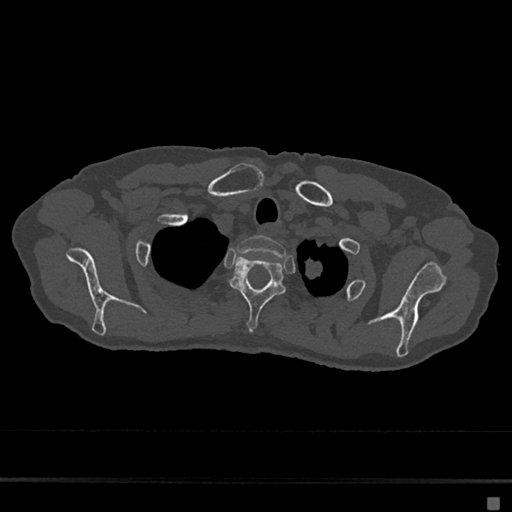
CT including the spine, one axial slice; bone window (W 1800 / L 400 HU); 0.5 mm slice thickness; 512 × 512 image matrix. Patient: female, 68 years. From the clinical record (not read from this slice): primary cancer: renal.
Annotated regions visible in this slice (semi-automatic segmentation, software-assisted and operator-edited):
- T1 vertebra: box from (x=237, y=235) to (x=286, y=257) px
- T2 vertebra: (x=230, y=255)–(x=286, y=331)
- T3 vertebra: (x=220, y=299)–(x=223, y=302)